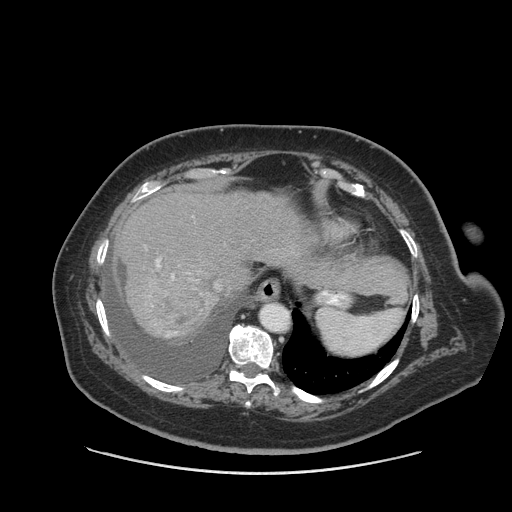
Contrast-enhanced abdominal CT (liver protocol), one axial slice. Position 69 of 91 along the scan axis. 140 kVp. Soft-tissue window (W 400 / L 40 HU). 2.5 mm slice thickness. 512 × 512 image matrix, field of view 420 × 420 mm. From the clinical record (not read from this slice): diagnosis: hepatocellular carcinoma (patient treated with transarterial chemoembolisation; whether this scan precedes or follows treatment is not stated here); TNM stage (as recorded): Stage-I; Child-Pugh class: A; tumour differentiation: well differentiated; tumour nodularity: uninodular.
Structures marked on this image (semi-automatic segmentation, software-assisted and operator-edited):
- liver parenchyma outside the tumour (the mass and vessels are separate outlines, so this box may not span the whole liver): bounding box (x1, y1, x2, y2) in pixels: (114, 186, 334, 338)
- mass: (144, 292, 209, 335)
- liver vessels: (156, 259, 174, 279)